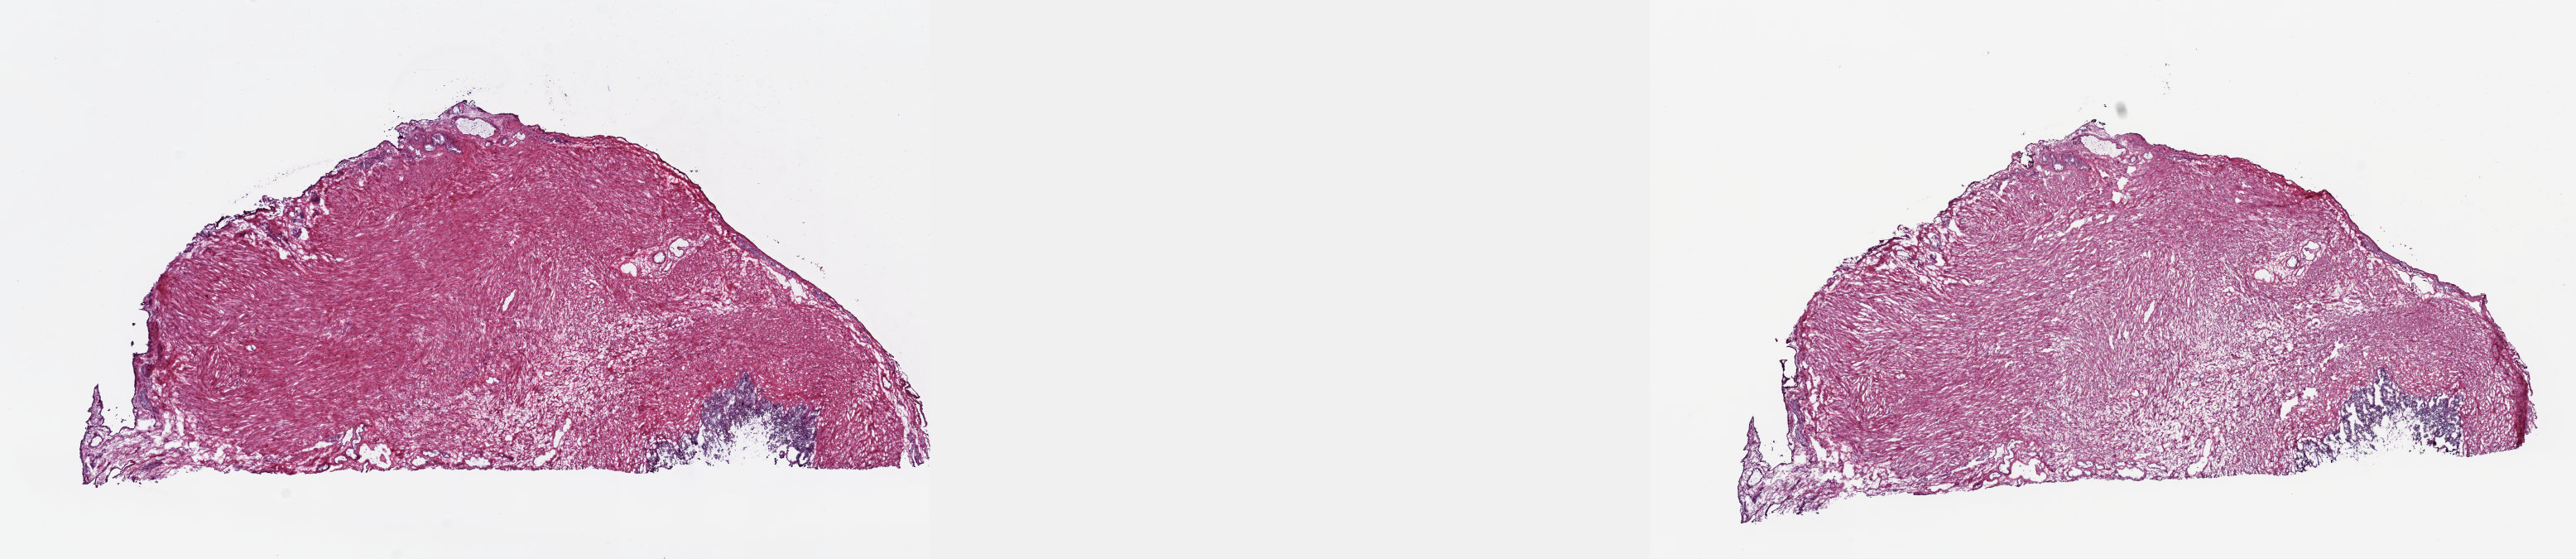
Whole-slide histology image, Hematoxylin and eosin (H&E) stained, whole scanned area (about 25.1 x 5.4 mm) shown as a low-resolution overview; frozen section from the top of the tissue portion; solid tissue normal (non-tumour tissue) sample from the prostate. Male, age 59 years at initial diagnosis. Composition of this section per pathologist review: tumour cells 0%, tumour nuclei 0%, normal cells 6%, stromal cells 94%, necrosis 0%. Infiltration values recorded for this section: lymphocyte infiltration 2%, monocyte infiltration 1%, neutrophil infiltration 1%.
This section: solid tissue normal sample (biorepository sample class). Patient diagnosis: Adenocarcinoma, NOS (prostate gland).